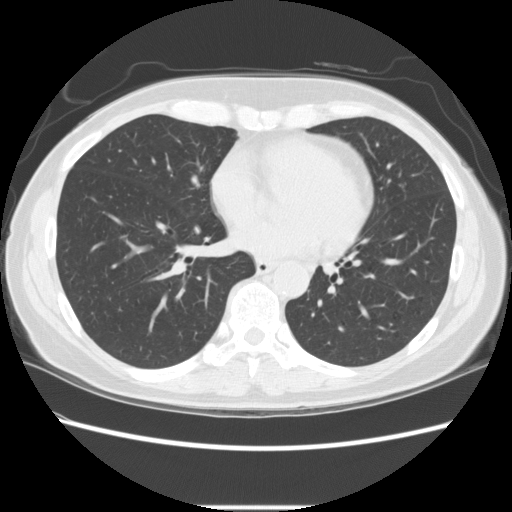
Chest CT (low-dose screening protocol), one axial image, first (baseline) screen, lung window (W 1500 / L -600 HU), 2.5 mm slice thickness, standard (soft-tissue) reconstruction kernel (STANDARD), 120 kVp, slice 145 of 256 in the series, 512 × 512 image matrix. Female participant, aged 60 years at enrolment. Current smoker at enrolment.
Lesion marked by an expert reader, bounding box <389,176,420,203> (left, top, right, bottom; pixels). Screening reader's record for this exam: no non-calcified nodule ≥4 mm recorded. Lung cancer was diagnosed 939 days after this screen (after the third annual screen): adenocarcinoma, NOS, lingula, poorly differentiated (G3), stage IA (AJCC 6th edition), 6 mm at pathology.